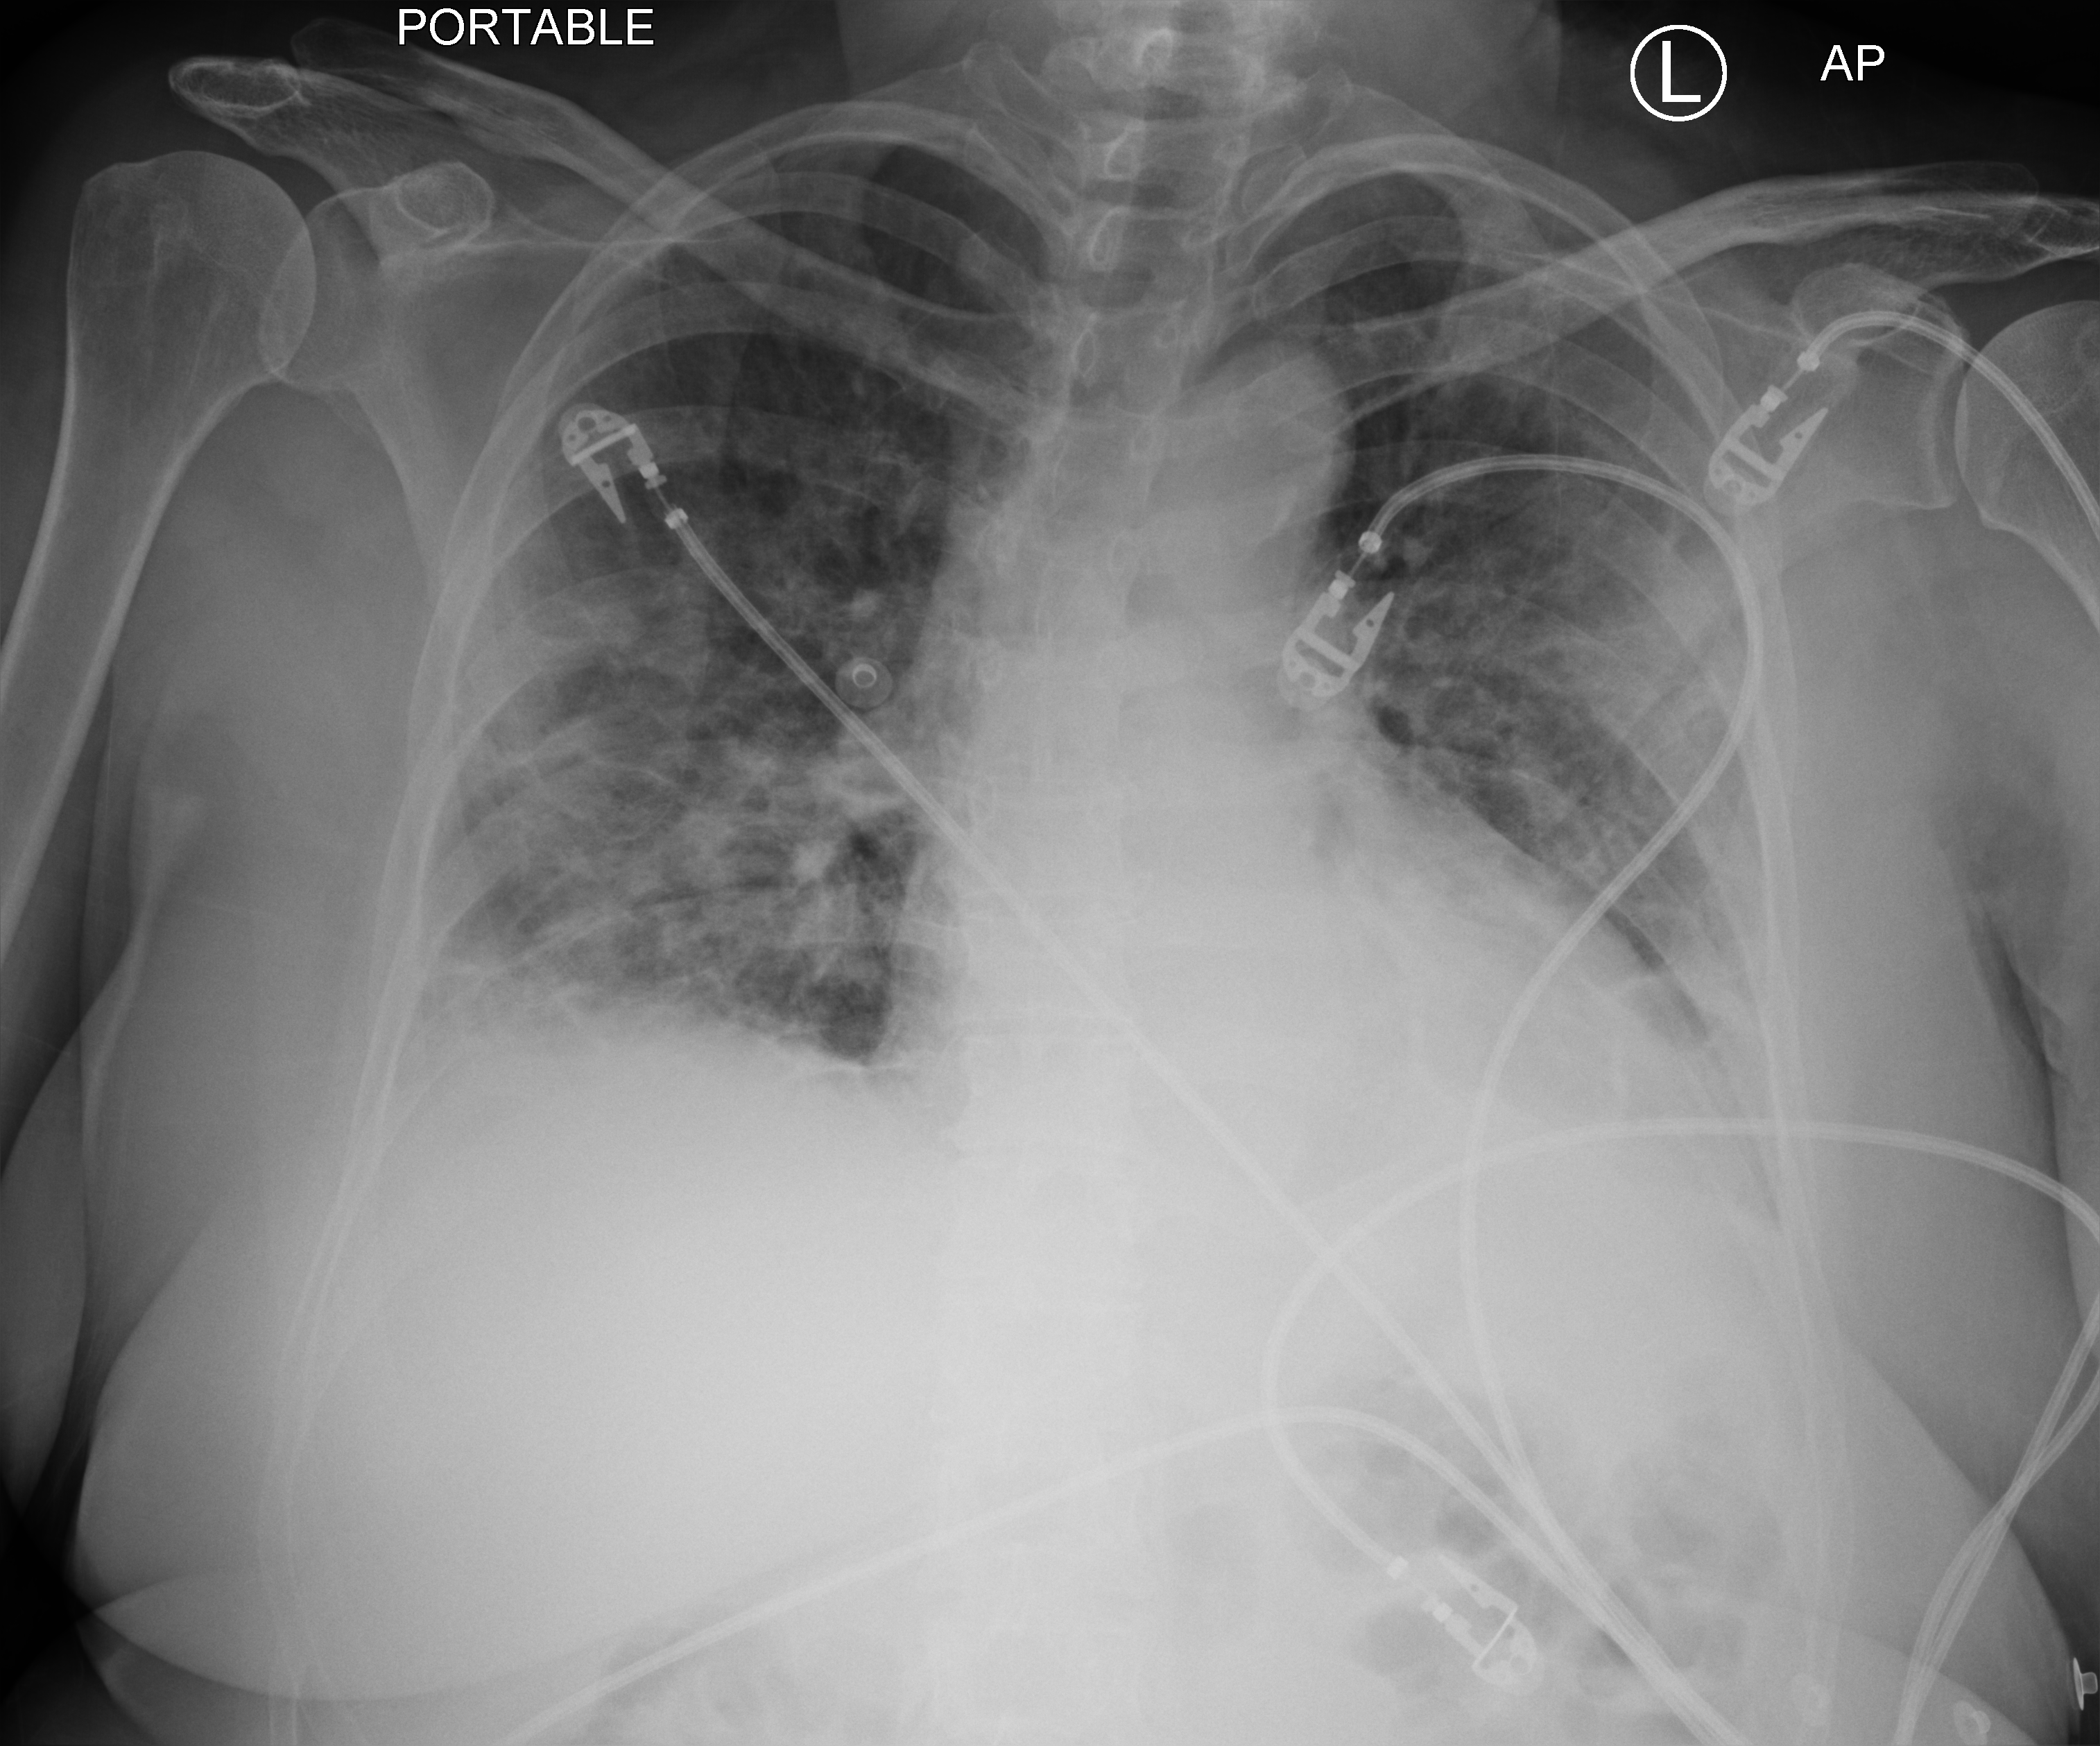
Portable chest radiograph, anteroposterior (AP) projection. Female patient hospitalised with COVID-19, age 60–74 years.
Hospital-stay facts (about this admission, not read from this image; timing relative to this image not recorded): admitted to intensive care during this hospital stay: no; mechanically ventilated during this hospital stay: no; hypertension (admission record): no.